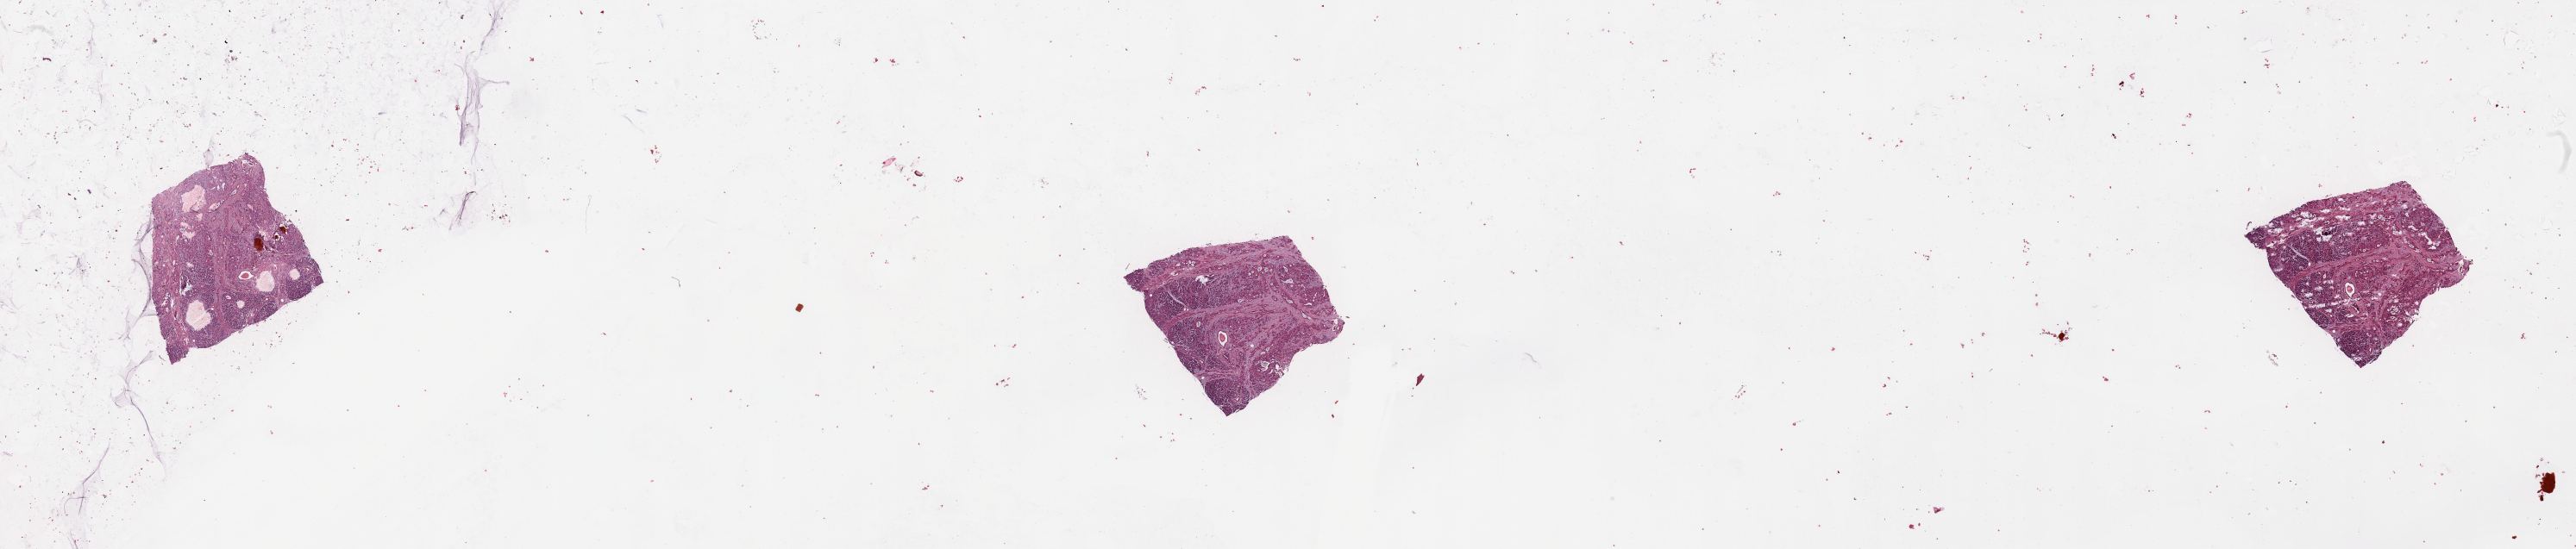
H&E-stained whole-slide image — whole scanned area (about 47.3 x 10.1 mm) shown as a low-resolution overview; tumour tissue sample, sampled site: pancreas. Female, 43 y/o. Histologic grade: G2 (moderately differentiated). Pathologist review of this section (percent, as recorded): tumour nuclei 20%, necrosis 1%.
• histologic diagnosis: Infiltrating duct carcinoma, NOS
• AJCC pathologic stage: III
• primary tumour site (as recorded): head